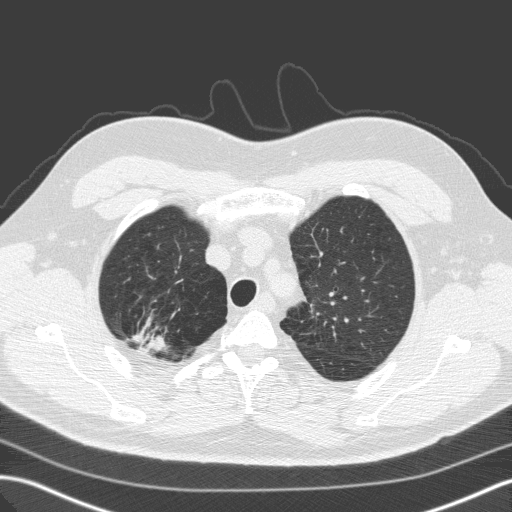
Axial slice from a low-dose chest CT screening exam. Baseline screening round. Lung window (W 1500 / L -600 HU). 2 mm slice thickness. Standard (soft-tissue) reconstruction kernel (C). Slice 25 of 149 in the series. Male, age 59 years at enrolment. Former smoker at enrolment.
Expert-annotated lung lesion, box from (x=118, y=314) to (x=181, y=366) px. Reader record for this screening exam (exam-level; its link to the box is not recorded): non-calcified nodule or mass ≥4 mm, right upper lobe, 28 × 25 mm, spiculated (stellate) margins, soft tissue attenuation. Lung cancer was diagnosed 64 days after this screen: large cell carcinoma, NOS, right upper lobe, undifferentiated (G4), stage IA (AJCC 6th edition), 25 mm at pathology.